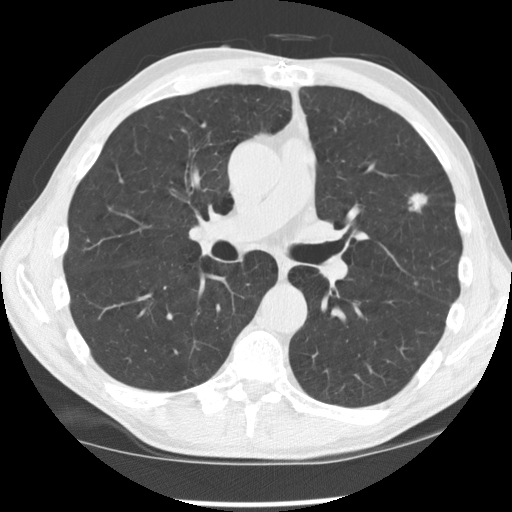
Low-dose screening chest CT, one axial slice; position 98 of 170 along the scan axis; lung window (W 1500 / L -600 HU); 2.5 mm slice thickness; 512 × 512 image matrix, field of view 340 × 340 mm.
Outlined on this slice (outlined manually by an expert reader):
- lesion 1 (tumor, upper lobe of left lung): box from (x=408, y=193) to (x=428, y=212) px